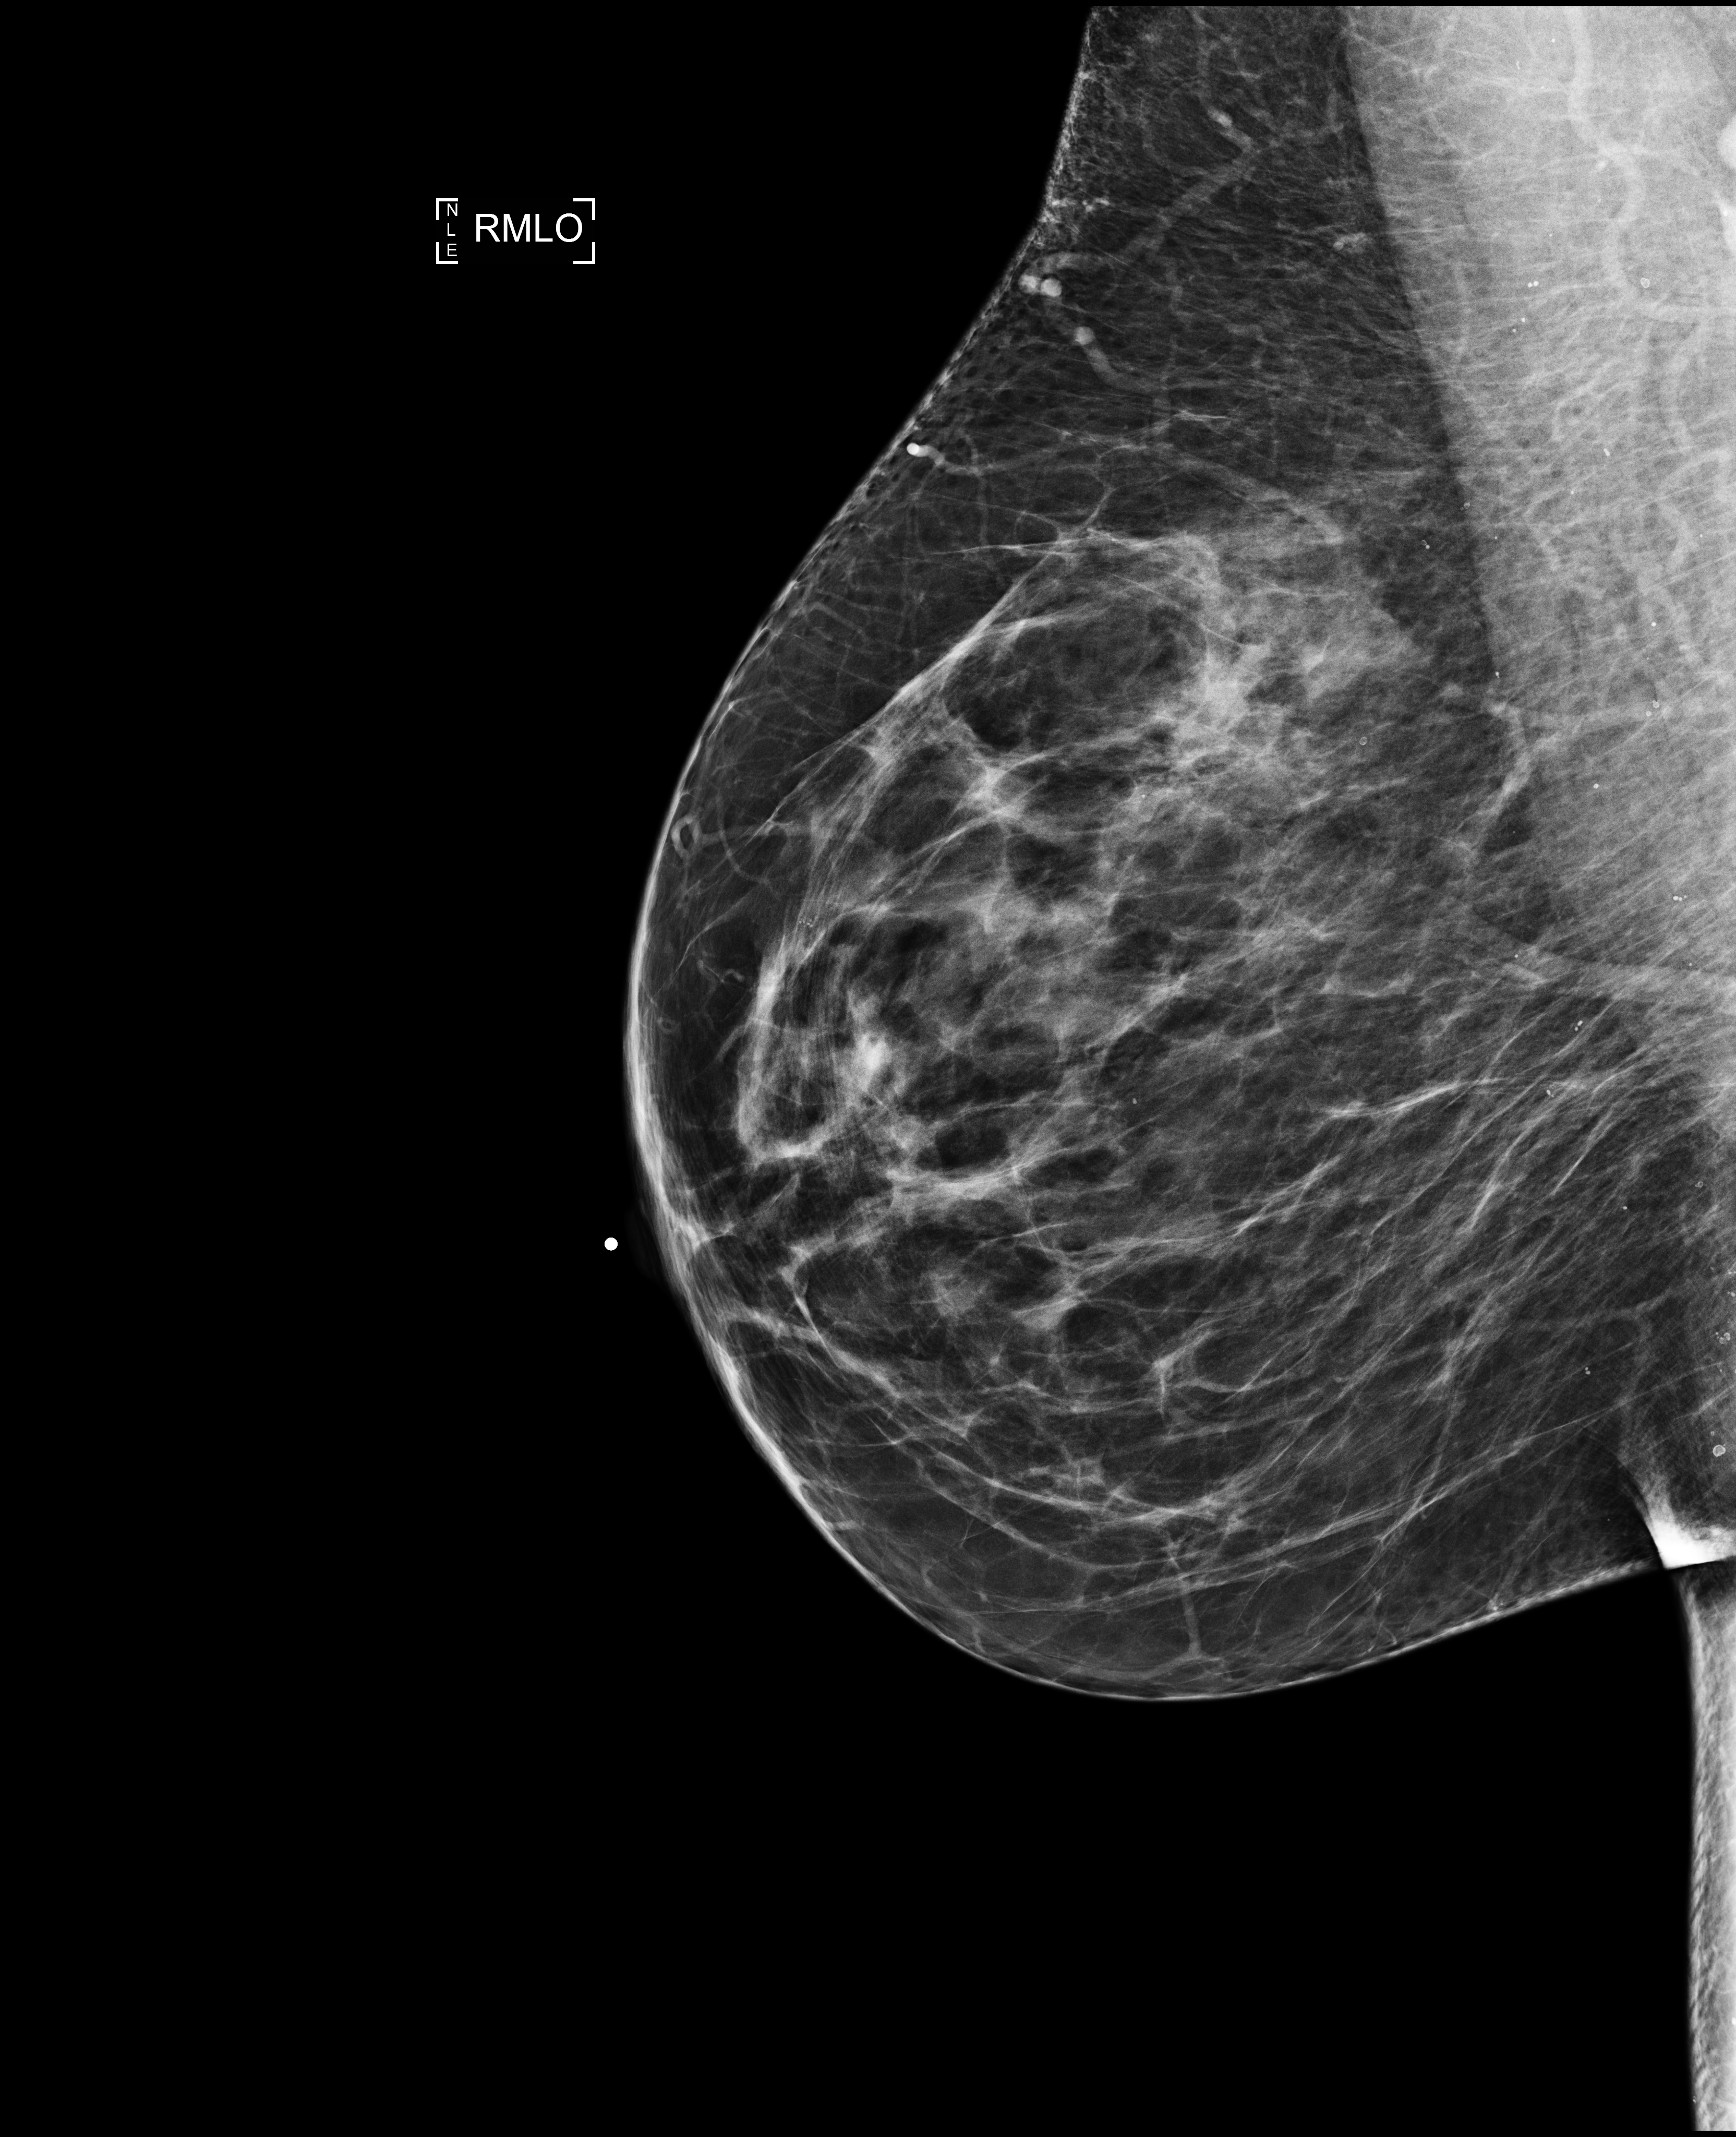
Annual screening mammography examination, system: Selenia Dimensions. Female patient, age 61 years.
Image type: full-field digital mammogram. Breast: right. Projection: medio-lateral oblique projection.